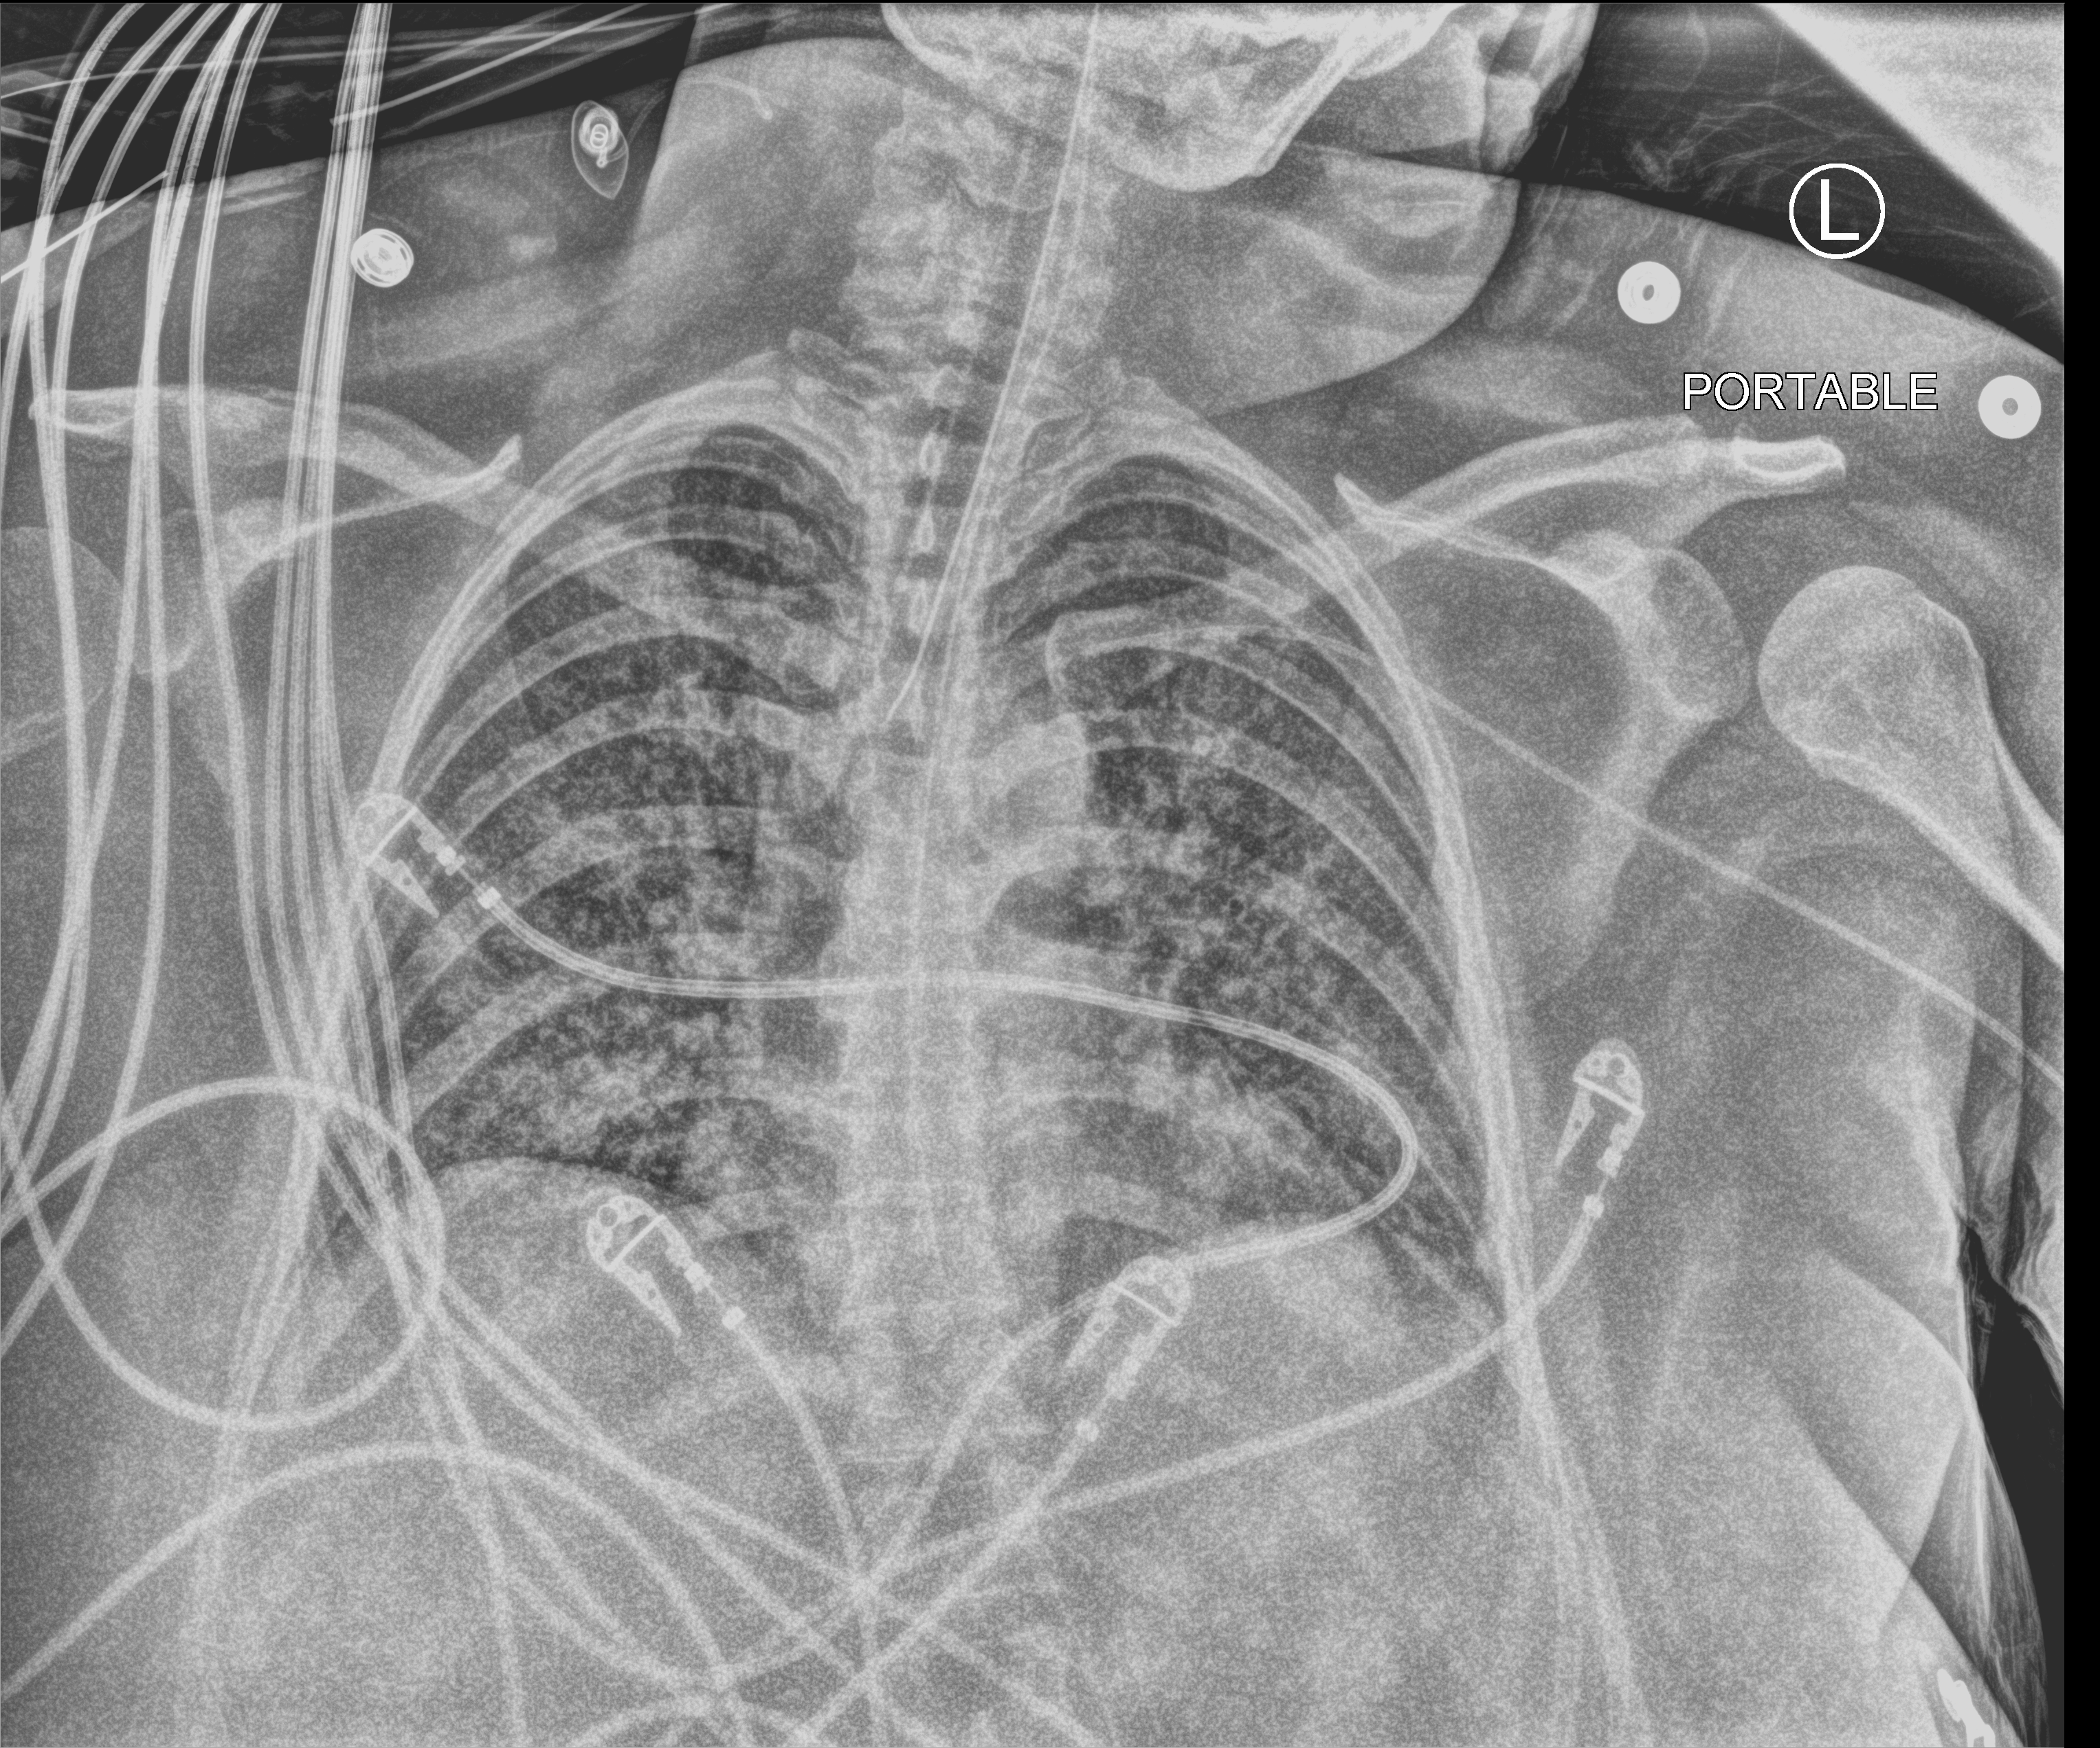
Bedside chest radiograph (computed radiography); anteroposterior (AP) projection. Female patient hospitalised with COVID-19, age 18–59 years.
Admission-level facts for this patient (not findings on this image; timing relative to this image not recorded): smoking status (admission record): never; diabetes (admission record): no; admitted to intensive care during this hospital stay: yes.